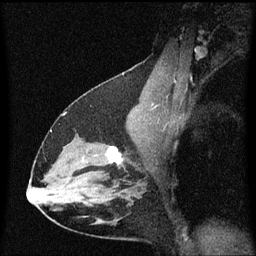
Breast MRI (dynamic contrast-enhanced), one sagittal slice; slice 37 of 60 in the series (ordered by position); dynamic contrast-enhanced series, image 2 of 3 at this slice position (ordered by acquisition); 1.5 T; TE 4.2 ms, TR 8.4 ms; 2 mm slice thickness; 256 × 256 image matrix, field of view 200 × 200 mm. Female patient, age 38 years. From the clinical record (not read from this slice): setting: breast cancer imaged before/during neoadjuvant chemotherapy; receptor status: HR-positive, HER2-negative.
Outlined on this slice (semi-automatic segmentation, software-assisted and operator-edited):
- analysis volume of interest (the breast-tissue region the enhancement analysis was run in; not a lesion): bounding box (x1, y1, x2, y2) in pixels: (94, 138, 141, 185)
- tumour enhancement mask (voxels above the 70 % enhancement threshold inside the analysis volume of interest): (108, 146, 123, 165)